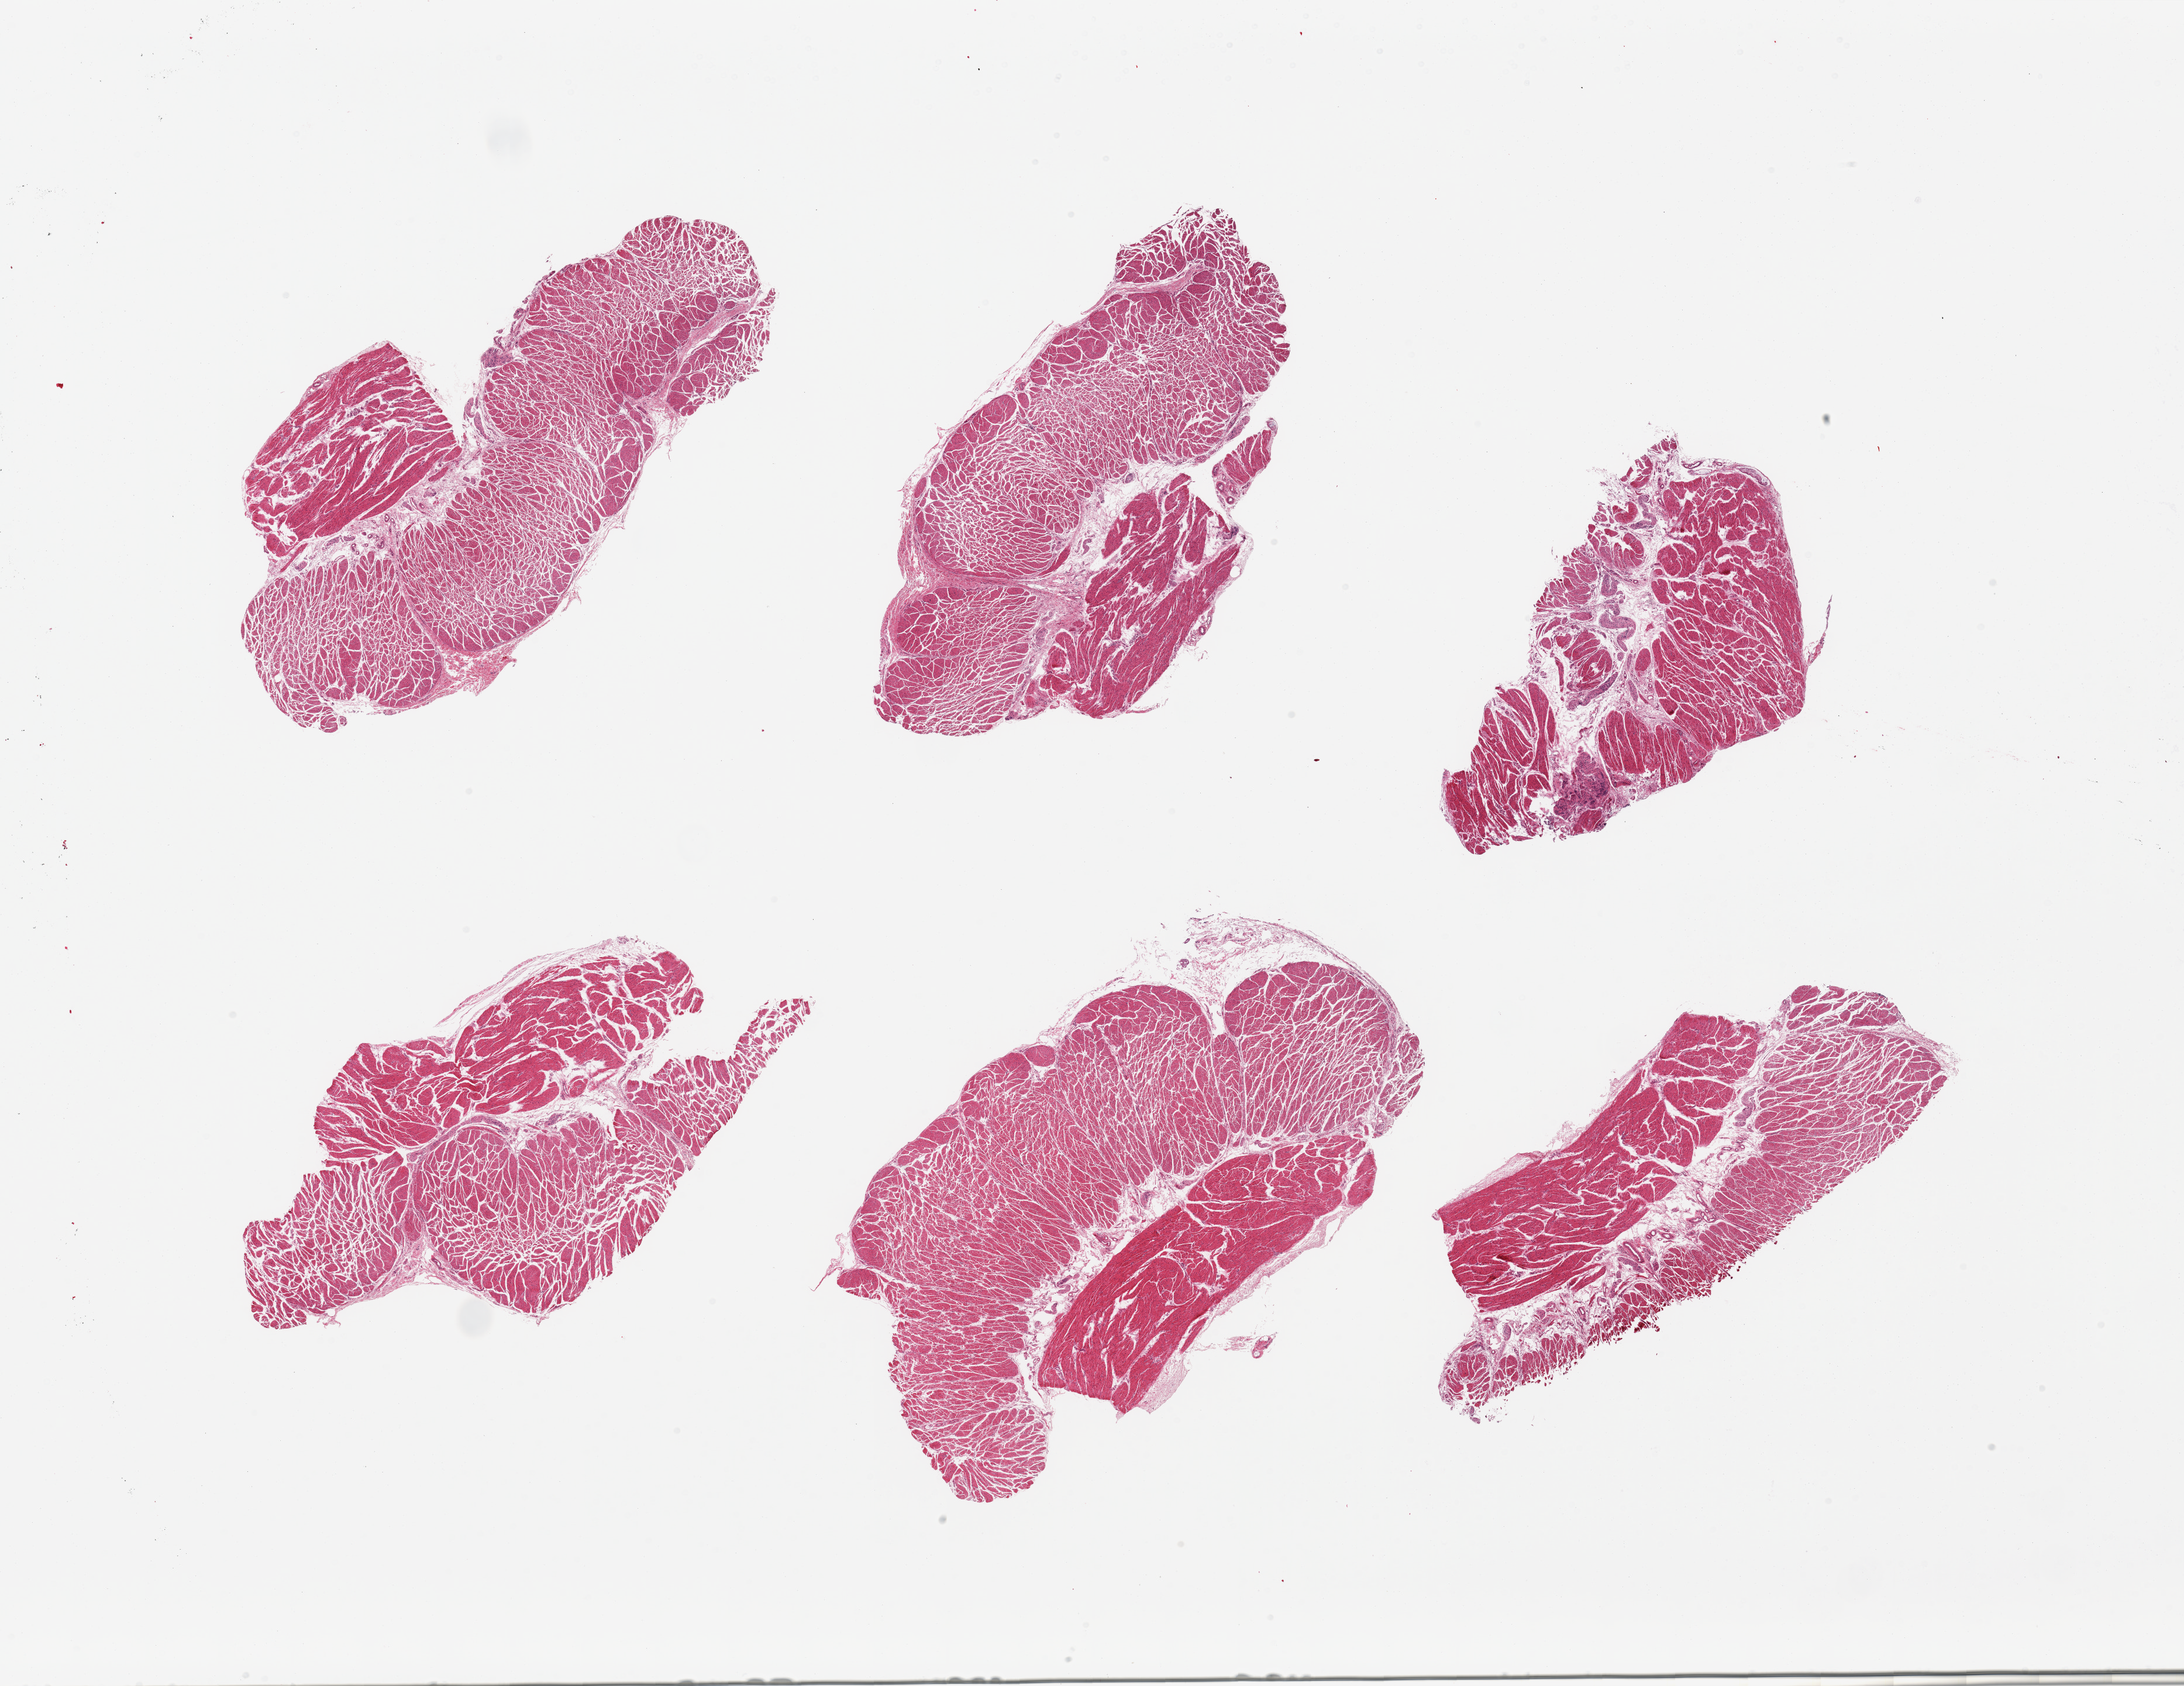
Digitized hematoxylin and eosin (H&E)-stained section, low-resolution overview of the scanned area, about 29.5 x 22.8 mm (from a 20x scan). PAXgene-fixed paraffin-embedded (PFPE) section. Section of esophageal muscle (target tissue). Tissue donor sample. Donor sex: female.
Pathologist's review note for this sample: 6 pieces, target muscularis, good specimens.